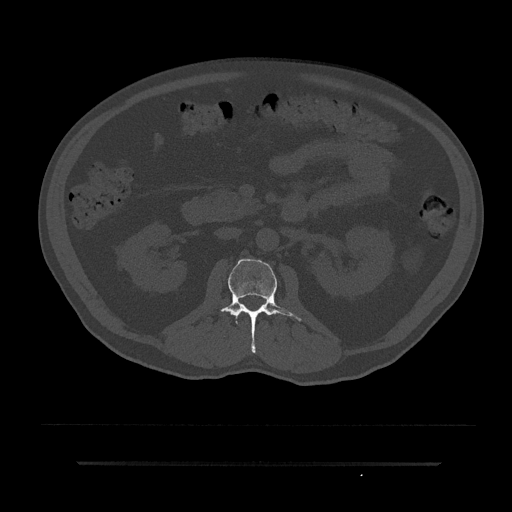
CT including the spine, one axial slice; position 77 of 797 along the scan axis; reconstruction kernel Br40s/3; 120 kVp; bone window (W 1800 / L 400 HU); 0.5 mm slice thickness; 512 × 512 image matrix. Patient: male, 59 years. From the clinical record (not read from this slice): primary cancer: bile ducts; vertebrae with lytic lesions (as recorded): T10.
Annotated regions visible in this slice (semi-automatic segmentation, software-assisted and operator-edited):
- L1 vertebra: bounding box (x1, y1, x2, y2) in pixels: (240, 311, 242, 313)
- L2 vertebra: (220, 258, 302, 353)